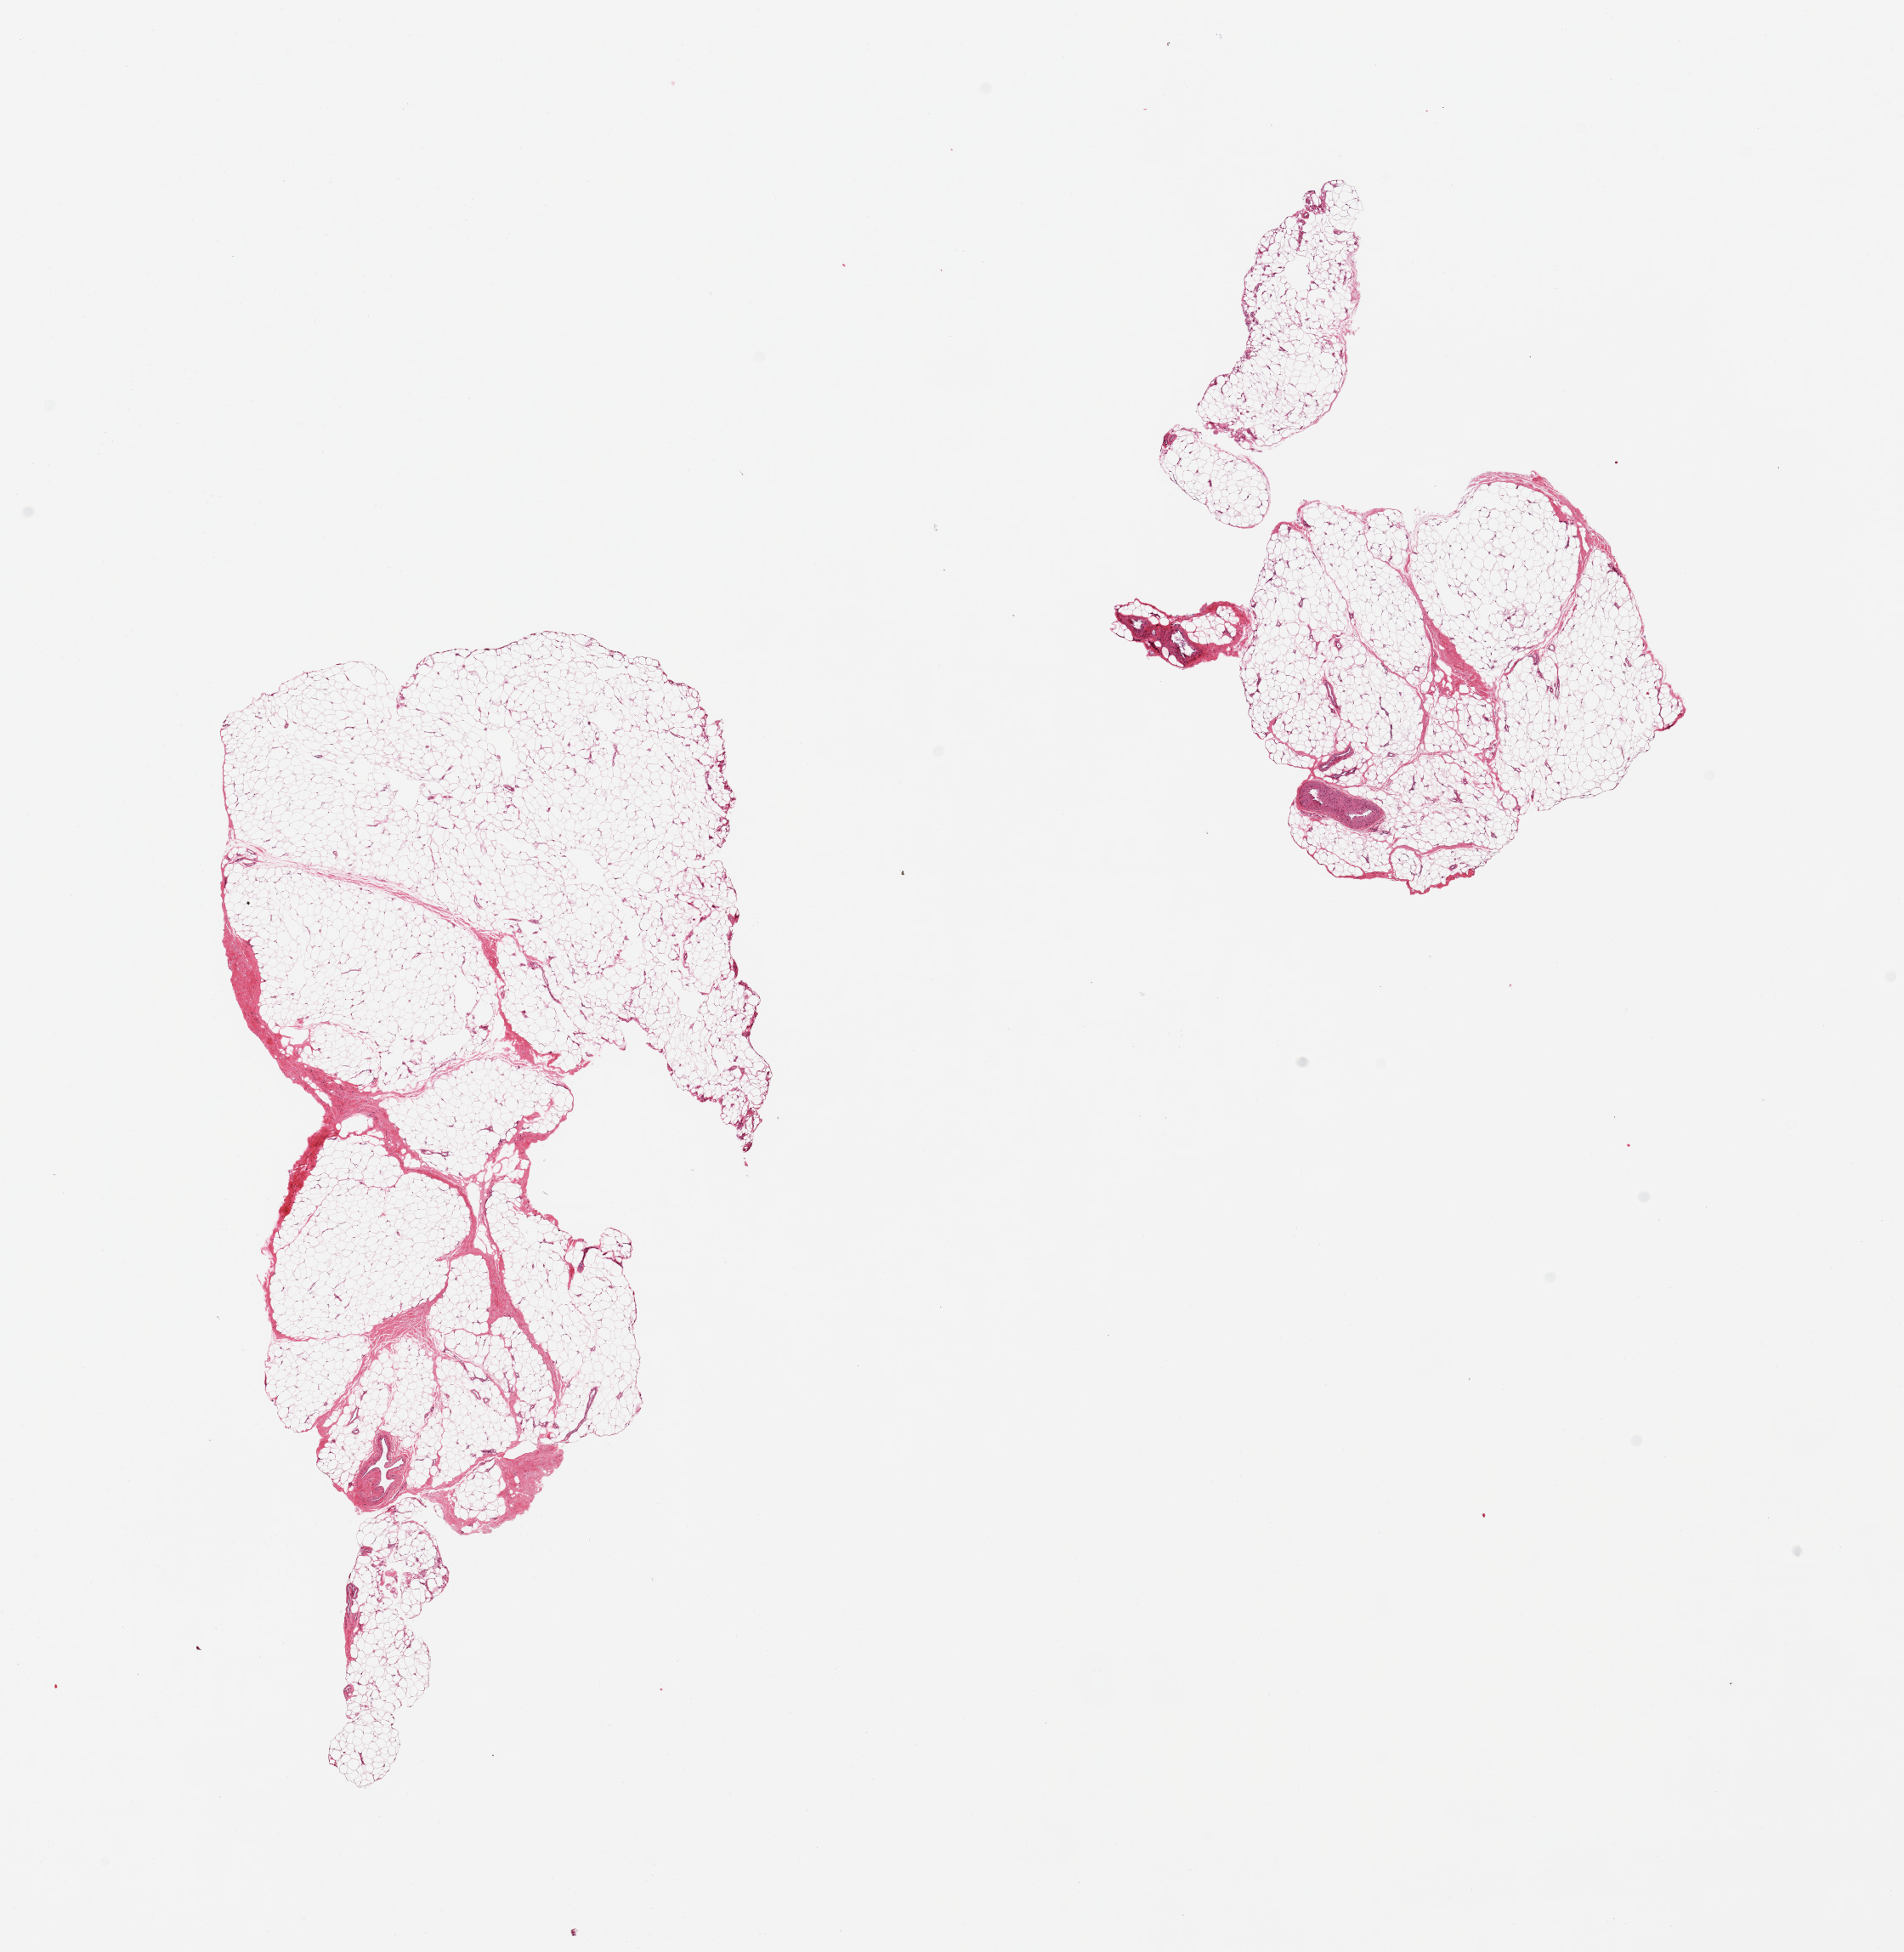
Digitized H&E-stained section, brightfield — a low-resolution overview of the entire scanned area, about 17.7 x 18.2 mm (from a 20x scan), PAXgene-fixed paraffin-embedded (PFPE) section, target tissue: adipose tissue, donor tissue sample. Male donor.
• review note (as recorded): 2 pieces, 5-10% fibrous/vascular tissue